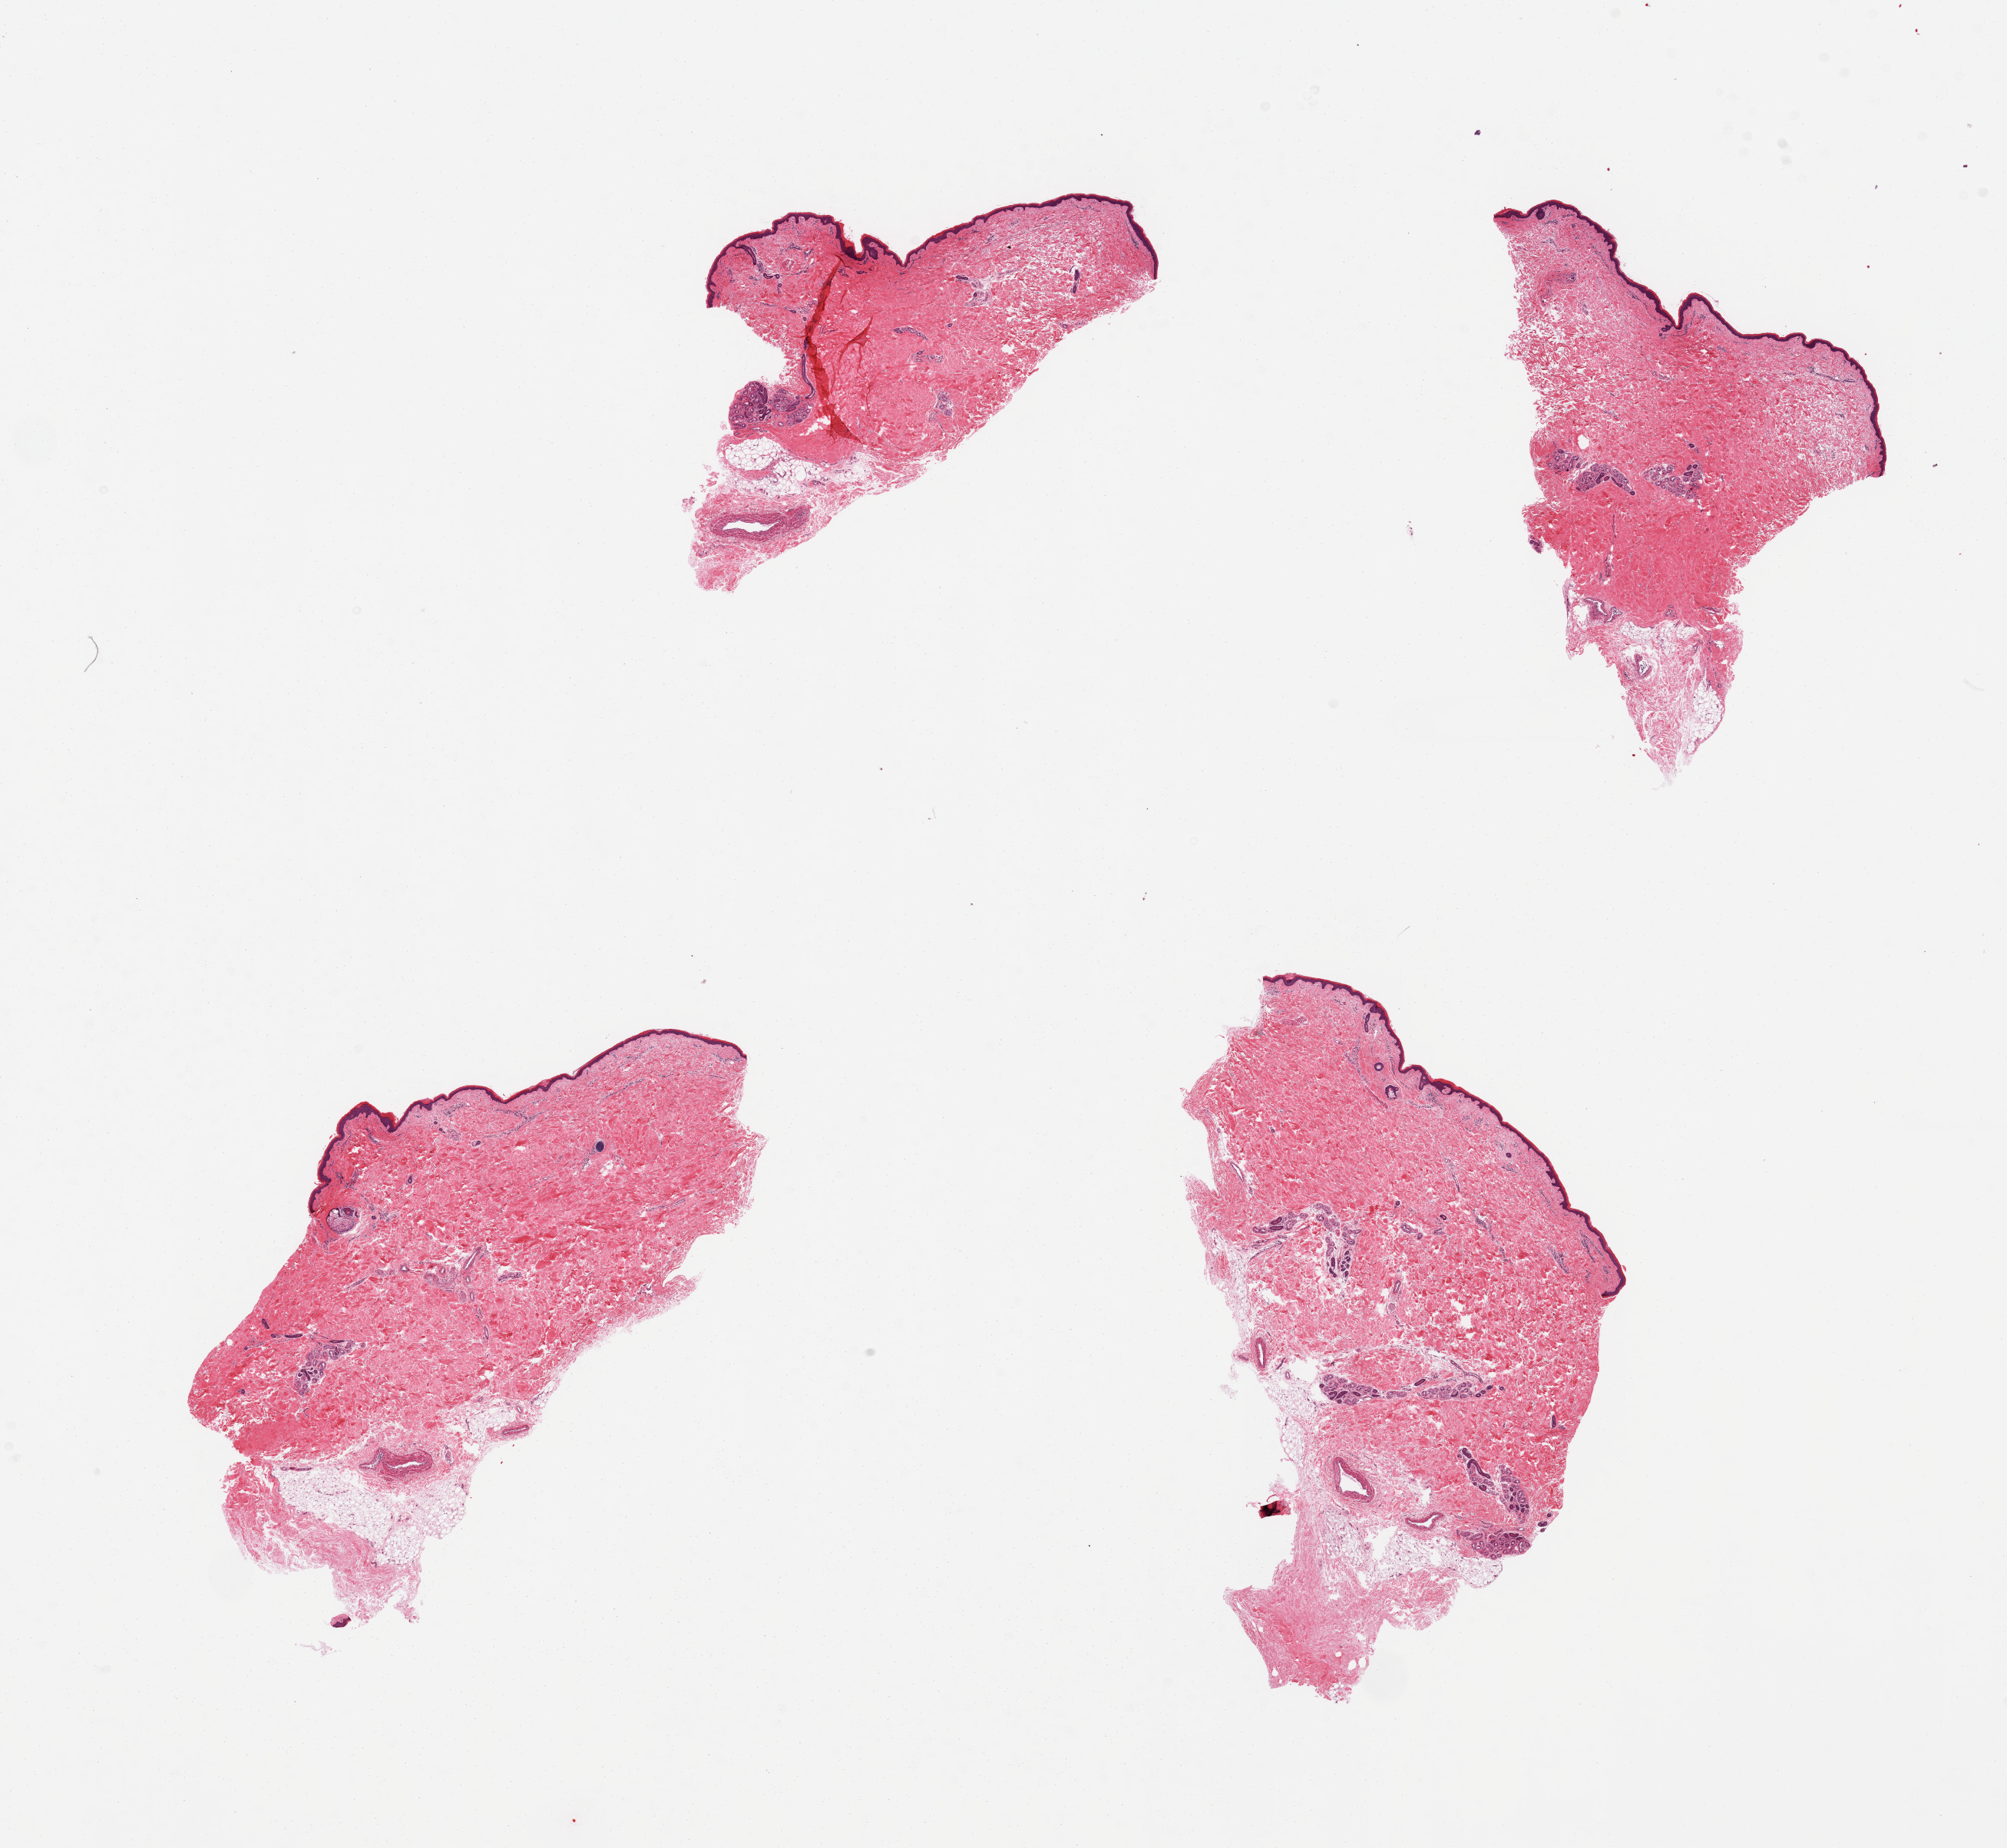
Hematoxylin and eosin (H&E) whole-slide image, shown as a low-resolution overview of the whole scanned area (about 20.7 x 19.0 mm, from a 20x scan), PAXgene-fixed paraffin-embedded (PFPE) section, sampled site (target tissue): skin of lower leg, tissue donor sample. Donor sex: male.
Reviewer comment on this tissue sample: 4 pieces; well trimmed.